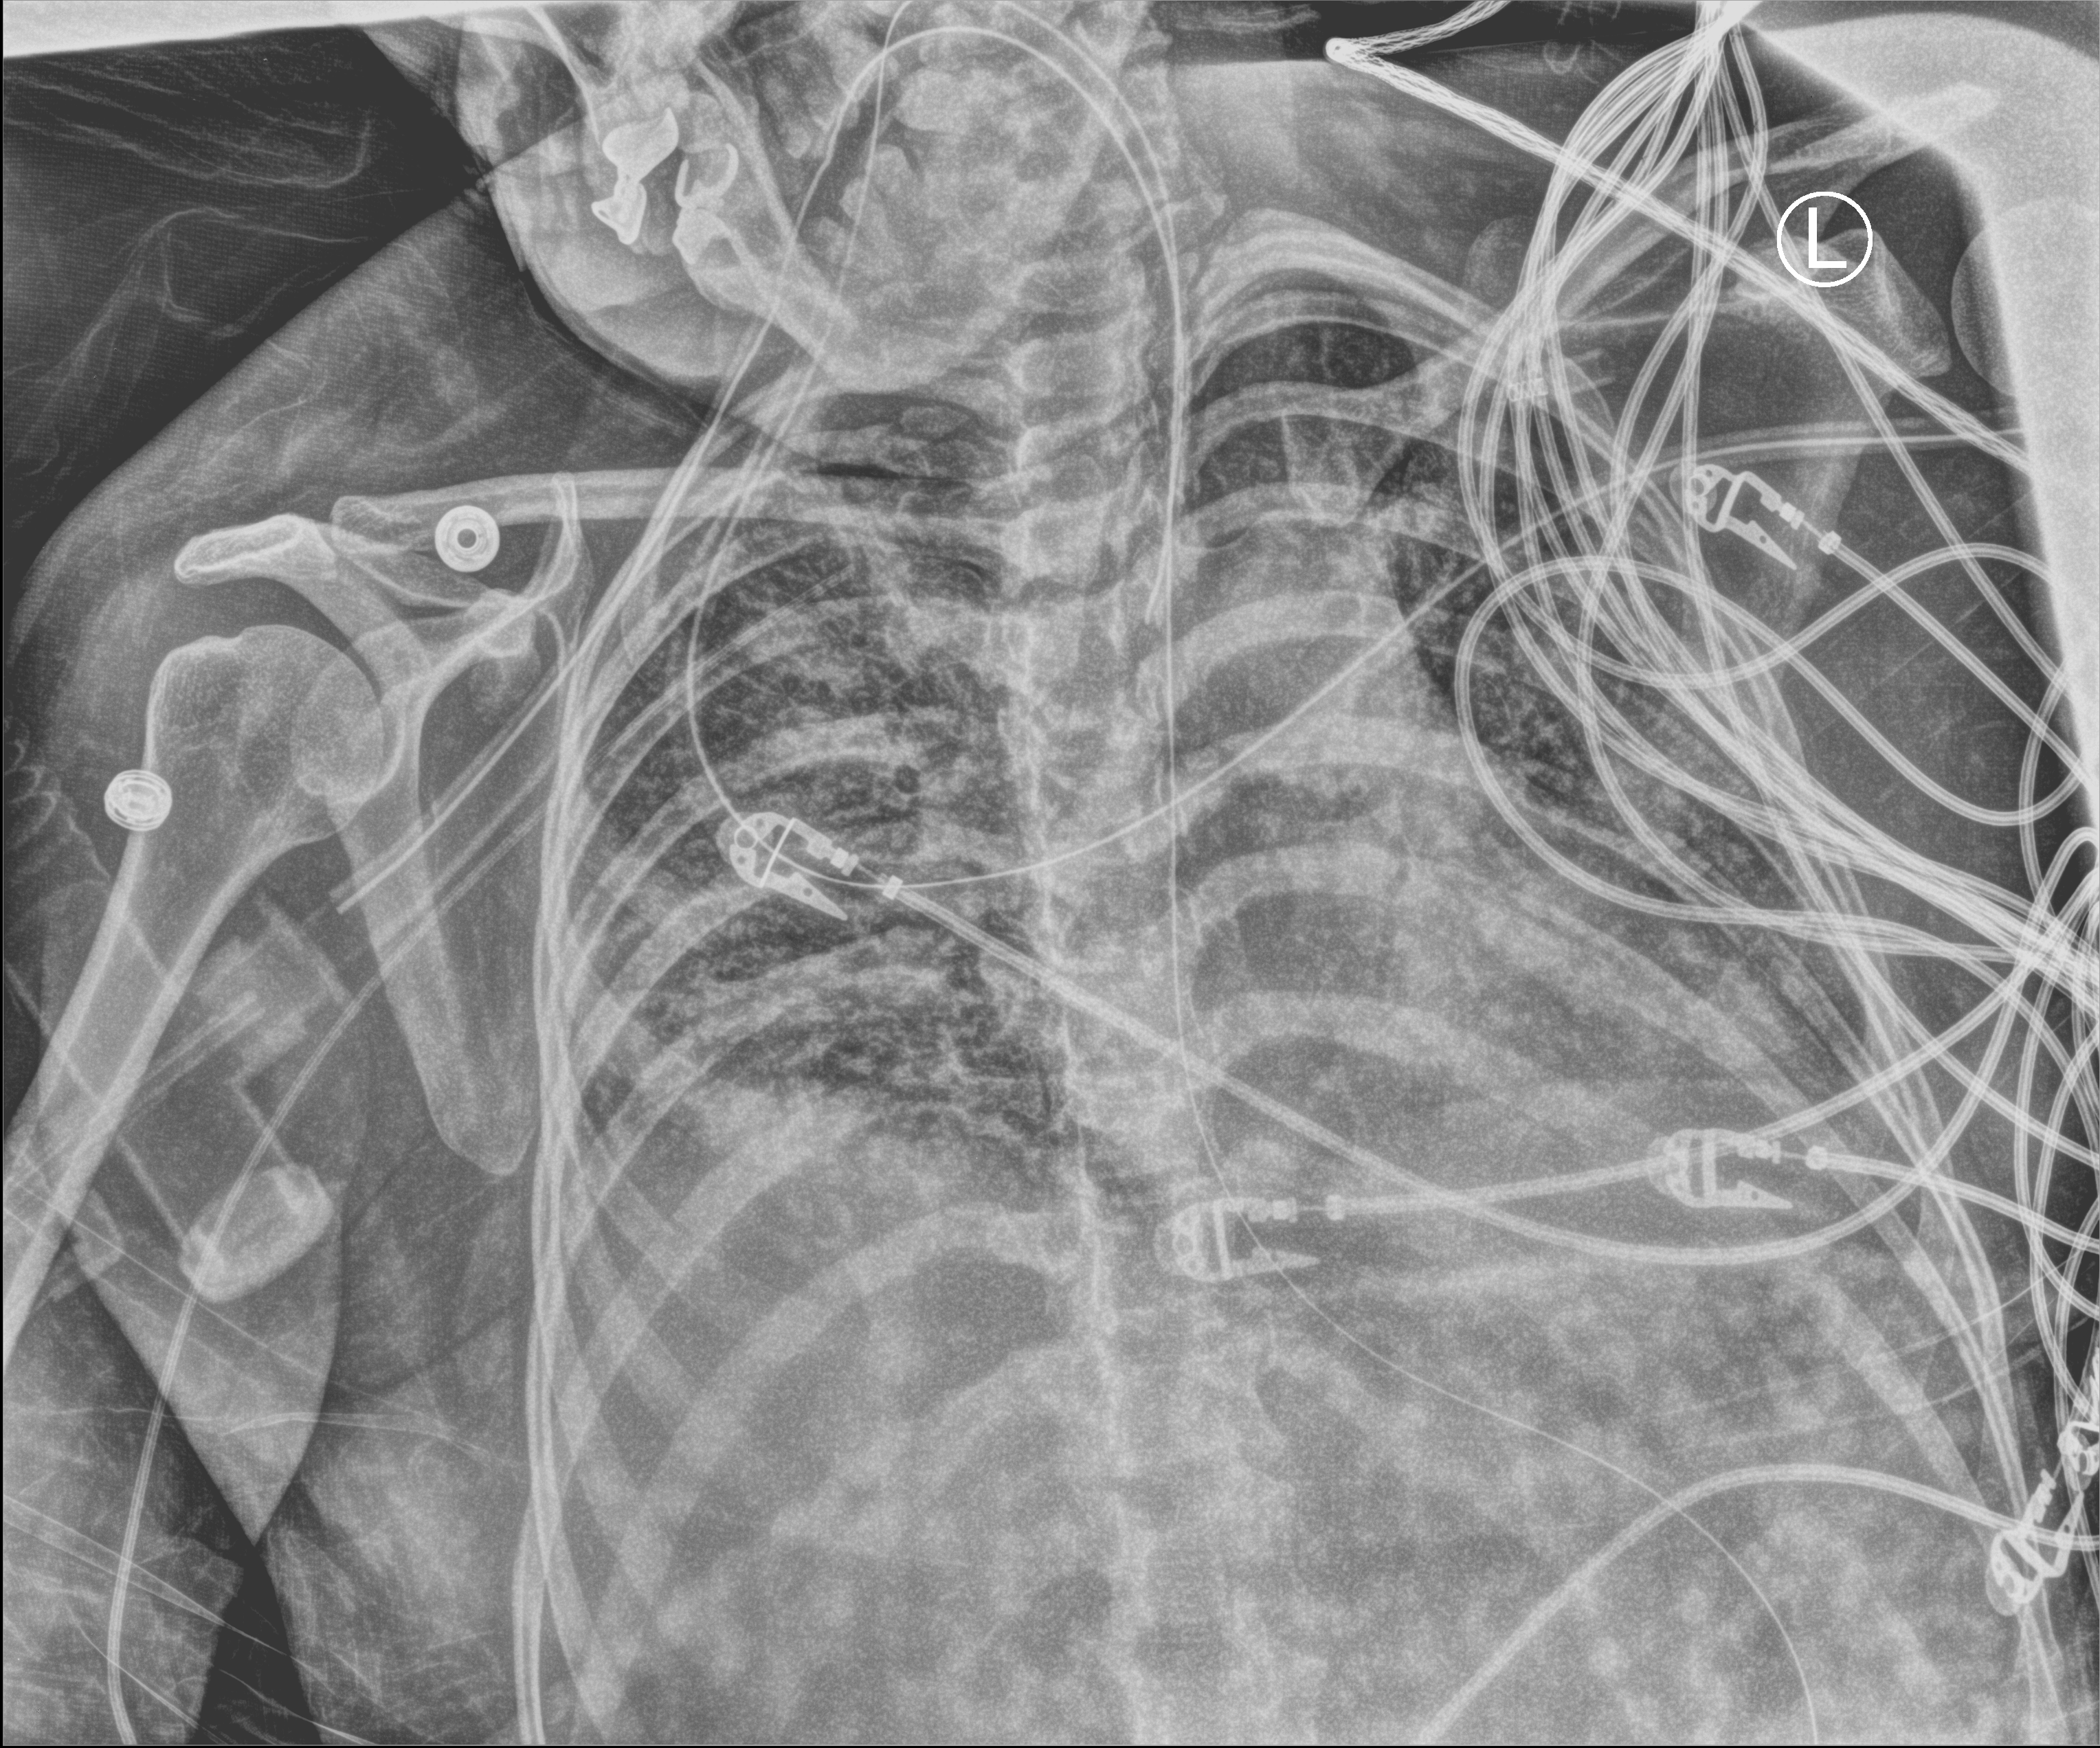
Chest X-ray (portable), anteroposterior (AP) projection. Female patient hospitalised with COVID-19, age 18–59 years.
Admission-level facts for this patient (not findings on this image; timing relative to this image not recorded): length of hospital stay: 71 days; mechanically ventilated during this hospital stay: yes.